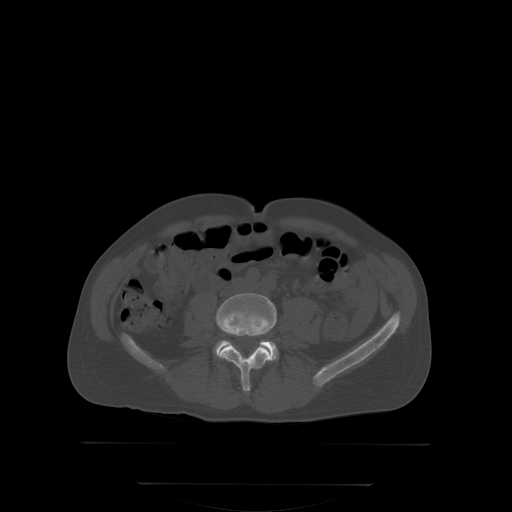
CT including the spine, one axial slice. Slice 104 of 350 in the series (ordered by position). Bone window (W 1800 / L 400 HU). 512 × 512 image matrix, field of view 500 × 500 mm. Patient: male, 58 years. Case-level facts recorded for this patient, not image findings: primary cancer: prostate; vertebrae with lytic lesions (as recorded): L1.
Annotated regions visible in this slice (semi-automatic segmentation, software-assisted and operator-edited):
- L4 vertebra: bounding box [x1, y1, x2, y2] px = [216, 293, 277, 392]
- L5 vertebra: [215, 340, 279, 360]